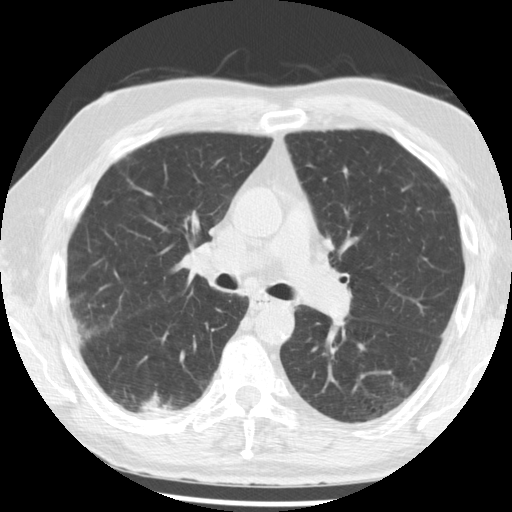
Axial slice from a low-dose chest CT screening exam; third screening round (two years after baseline); lung window (W 1500 / L -600 HU); 2.5 mm slice thickness; standard (soft-tissue) reconstruction kernel (STANDARD); 120 kVp; slice 124 of 221 in the series. Male, age 68 years at enrolment. Current smoker at enrolment.
Lesion marked by an expert reader, bounding box [x1, y1, x2, y2] px = [116, 377, 196, 434]. The screening reader recorded 3 non-calcified nodules or masses ≥4 mm on this exam (right lower lobe, right lower lobe, right lower lobe); which of them this box marks is not recorded. Official screen result: positive, other. Lung cancer was diagnosed 48 days after this screen: squamous cell carcinoma, NOS, right lower lobe, moderately differentiated (G2), stage IB (AJCC 6th edition), 20 mm at pathology.